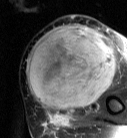
MRI of an extremity soft-tissue mass, one axial slice; position 30 of 87 along the scan axis; T2-weighted fat-saturated; MR volume resampled by the dataset authors to the PET/CT grid (not the native acquisition matrix); 3.27 mm slice thickness; 127 × 138 image matrix. Female patient. Case-level facts recorded for this patient, not image findings: histological type: pleiomorphic leiomyosarcoma; grade: high; site of the primary tumour: left biceps.
Structures marked on this image (expert contour drawn on MRI and transferred to this co-registered scan by the dataset authors):
- gross tumour volume including surrounding oedema: bounding box (x1, y1, x2, y2) in pixels: (25, 25, 115, 113)
- gross tumour volume (mass): (25, 25, 115, 111)